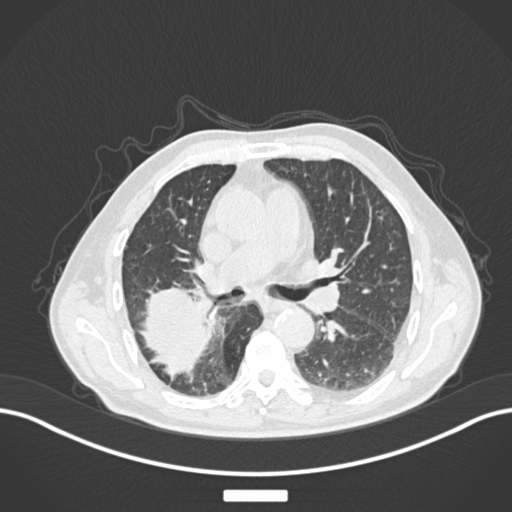
Chest CT, one axial slice; position 99 of 201 along the scan axis; reconstruction kernel B30f; lung window (W 1500 / L -600 HU); 1 mm slice thickness; 512 × 512 image matrix, field of view 400 × 400 mm. Patient: male, 72 years. Case-level facts recorded for this patient, not image findings: clinical TNM (as recorded): T3 N2 M0.
Structures marked on this image (bounding box drawn by a radiologist):
- lung tumour (recorded histology: adenocarcinoma): bounding box <139,284,222,382> (left, top, right, bottom; pixels)